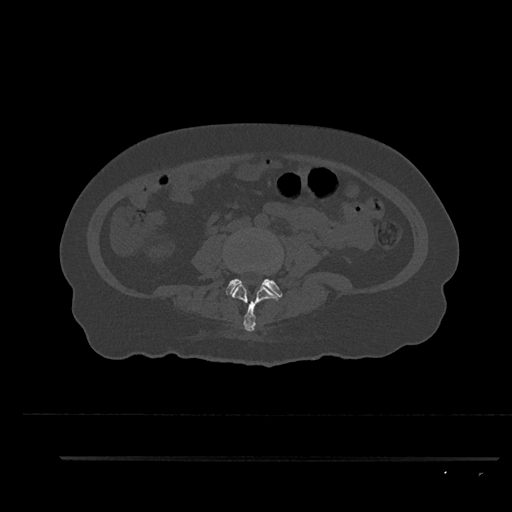
CT including the spine, one axial slice. Bone window (W 1800 / L 400 HU). 0.5 mm slice thickness. 512 × 512 image matrix, field of view 408 × 408 mm. Patient: female, 44 years. From the clinical record (not read from this slice): primary cancer: renal; vertebrae with lytic lesions (as recorded): L1.
Structures marked on this image (semi-automatically segmented with operator editing):
- L3 vertebra: bounding box (x1, y1, x2, y2) in pixels: (232, 284, 281, 331)
- L4 vertebra: (225, 235, 282, 297)